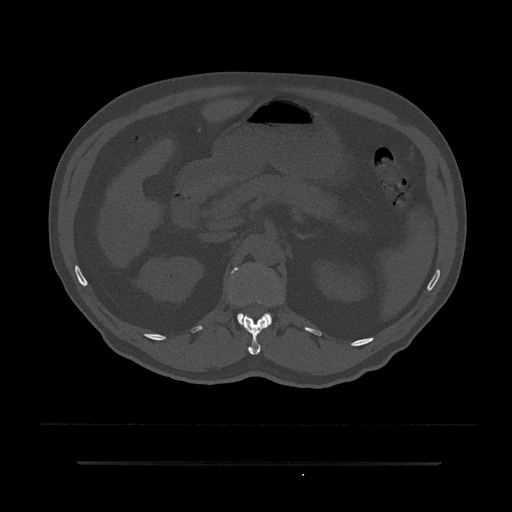
CT including the spine, one axial slice; position 182 of 797 along the scan axis; reconstruction kernel Br40s/3; 120 kVp; bone window (W 1800 / L 400 HU); 0.5 mm slice thickness; 512 × 512 image matrix, field of view 464 × 464 mm. Patient: male, 59 years. Case-level facts recorded for this patient, not image findings: primary cancer: bile ducts; vertebrae with lytic lesions (as recorded): T10.
Structures marked on this image (semi-automatically segmented with operator editing):
- L1 vertebra: bounding box (x1, y1, x2, y2) in pixels: (232, 267, 272, 324)
- T12 vertebra: (241, 297, 283, 355)